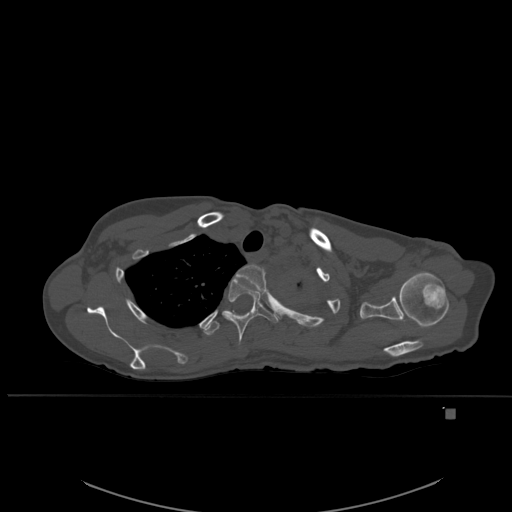
CT including the spine, one axial slice; slice 425 of 537 in the series (ordered by position); bone window (W 1800 / L 400 HU); 1.5 mm slice thickness; 512 × 512 image matrix, field of view 440 × 440 mm. Female patient, age 45 years. Case-level facts recorded for this patient, not image findings: primary cancer: lung.
Annotated regions visible in this slice (semi-automatic segmentation, software-assisted and operator-edited):
- T2 vertebra: bounding box <234,264,267,294> (left, top, right, bottom; pixels)
- T3 vertebra: <224,277,278,347>
- T4 vertebra: <202,311,228,336>